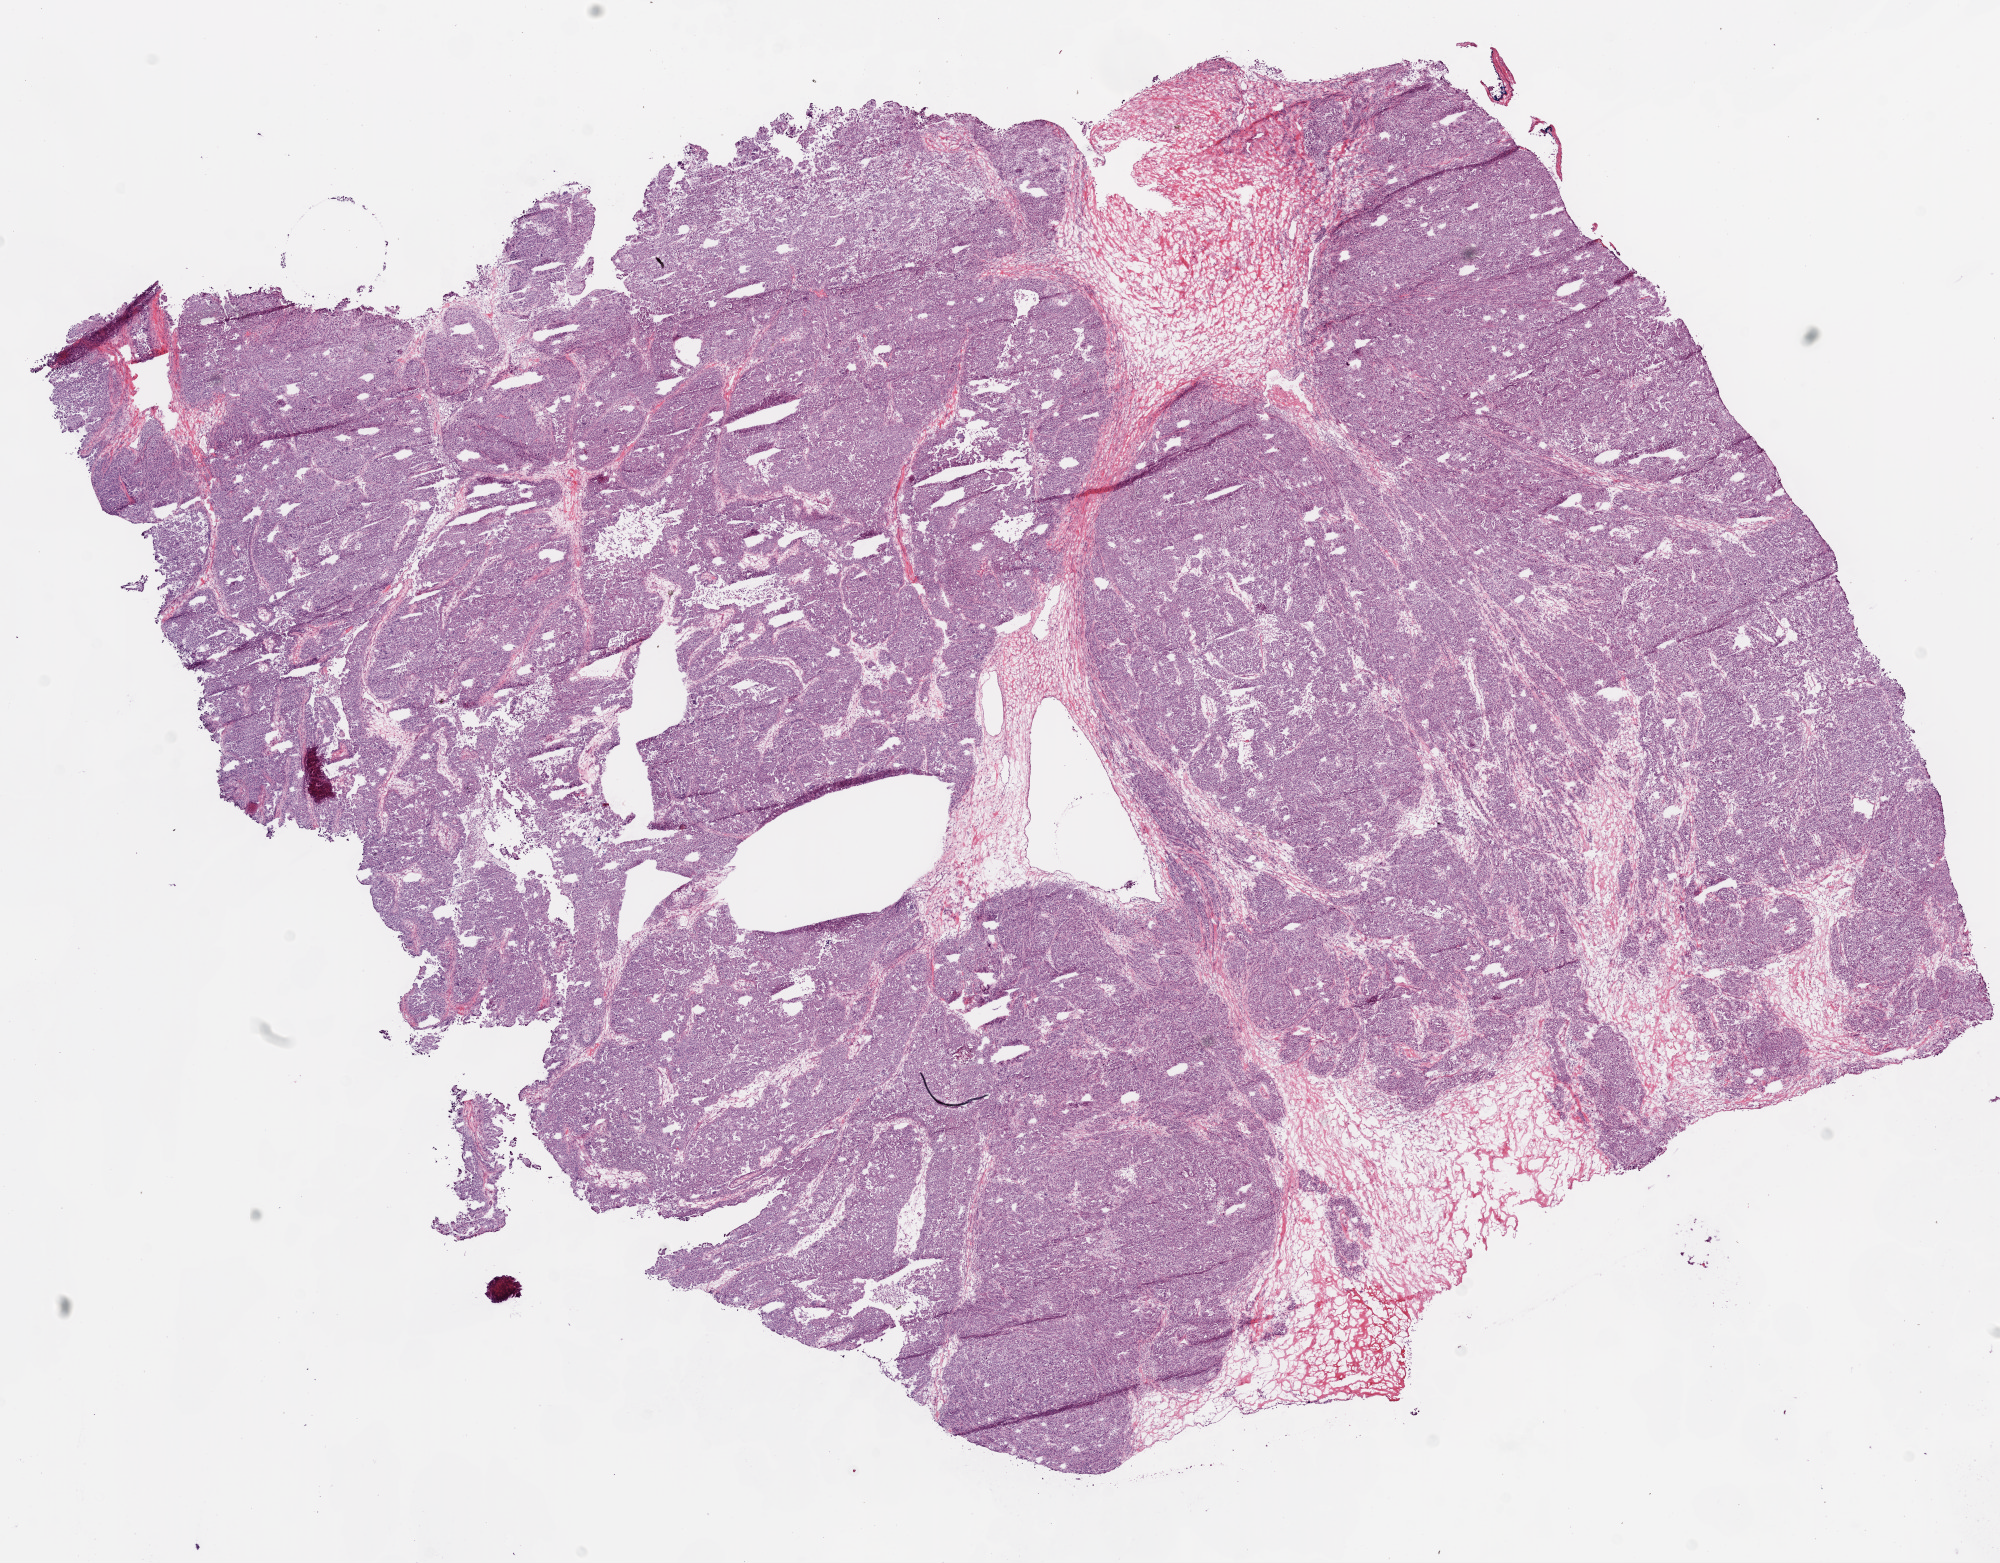
Digitized H&E-stained tissue section (whole slide) — whole scanned area (about 16.0 x 12.5 mm) shown as a low-resolution overview, frozen section, sample: primary tumour, ovary. Female patient; age at initial diagnosis 55 years. Histologic grade: G3 (poorly differentiated). Pathologist review of this section (percent, as recorded): tumour cells 90%, tumour nuclei 75%, normal cells 0%, stromal cells 10%, necrosis 0%. Inflammatory infiltration, as recorded: lymphocyte infiltration 20%.
FIGO stage: IIIC. Laterality: right. Pathologic diagnosis: Serous cystadenocarcinoma, NOS.